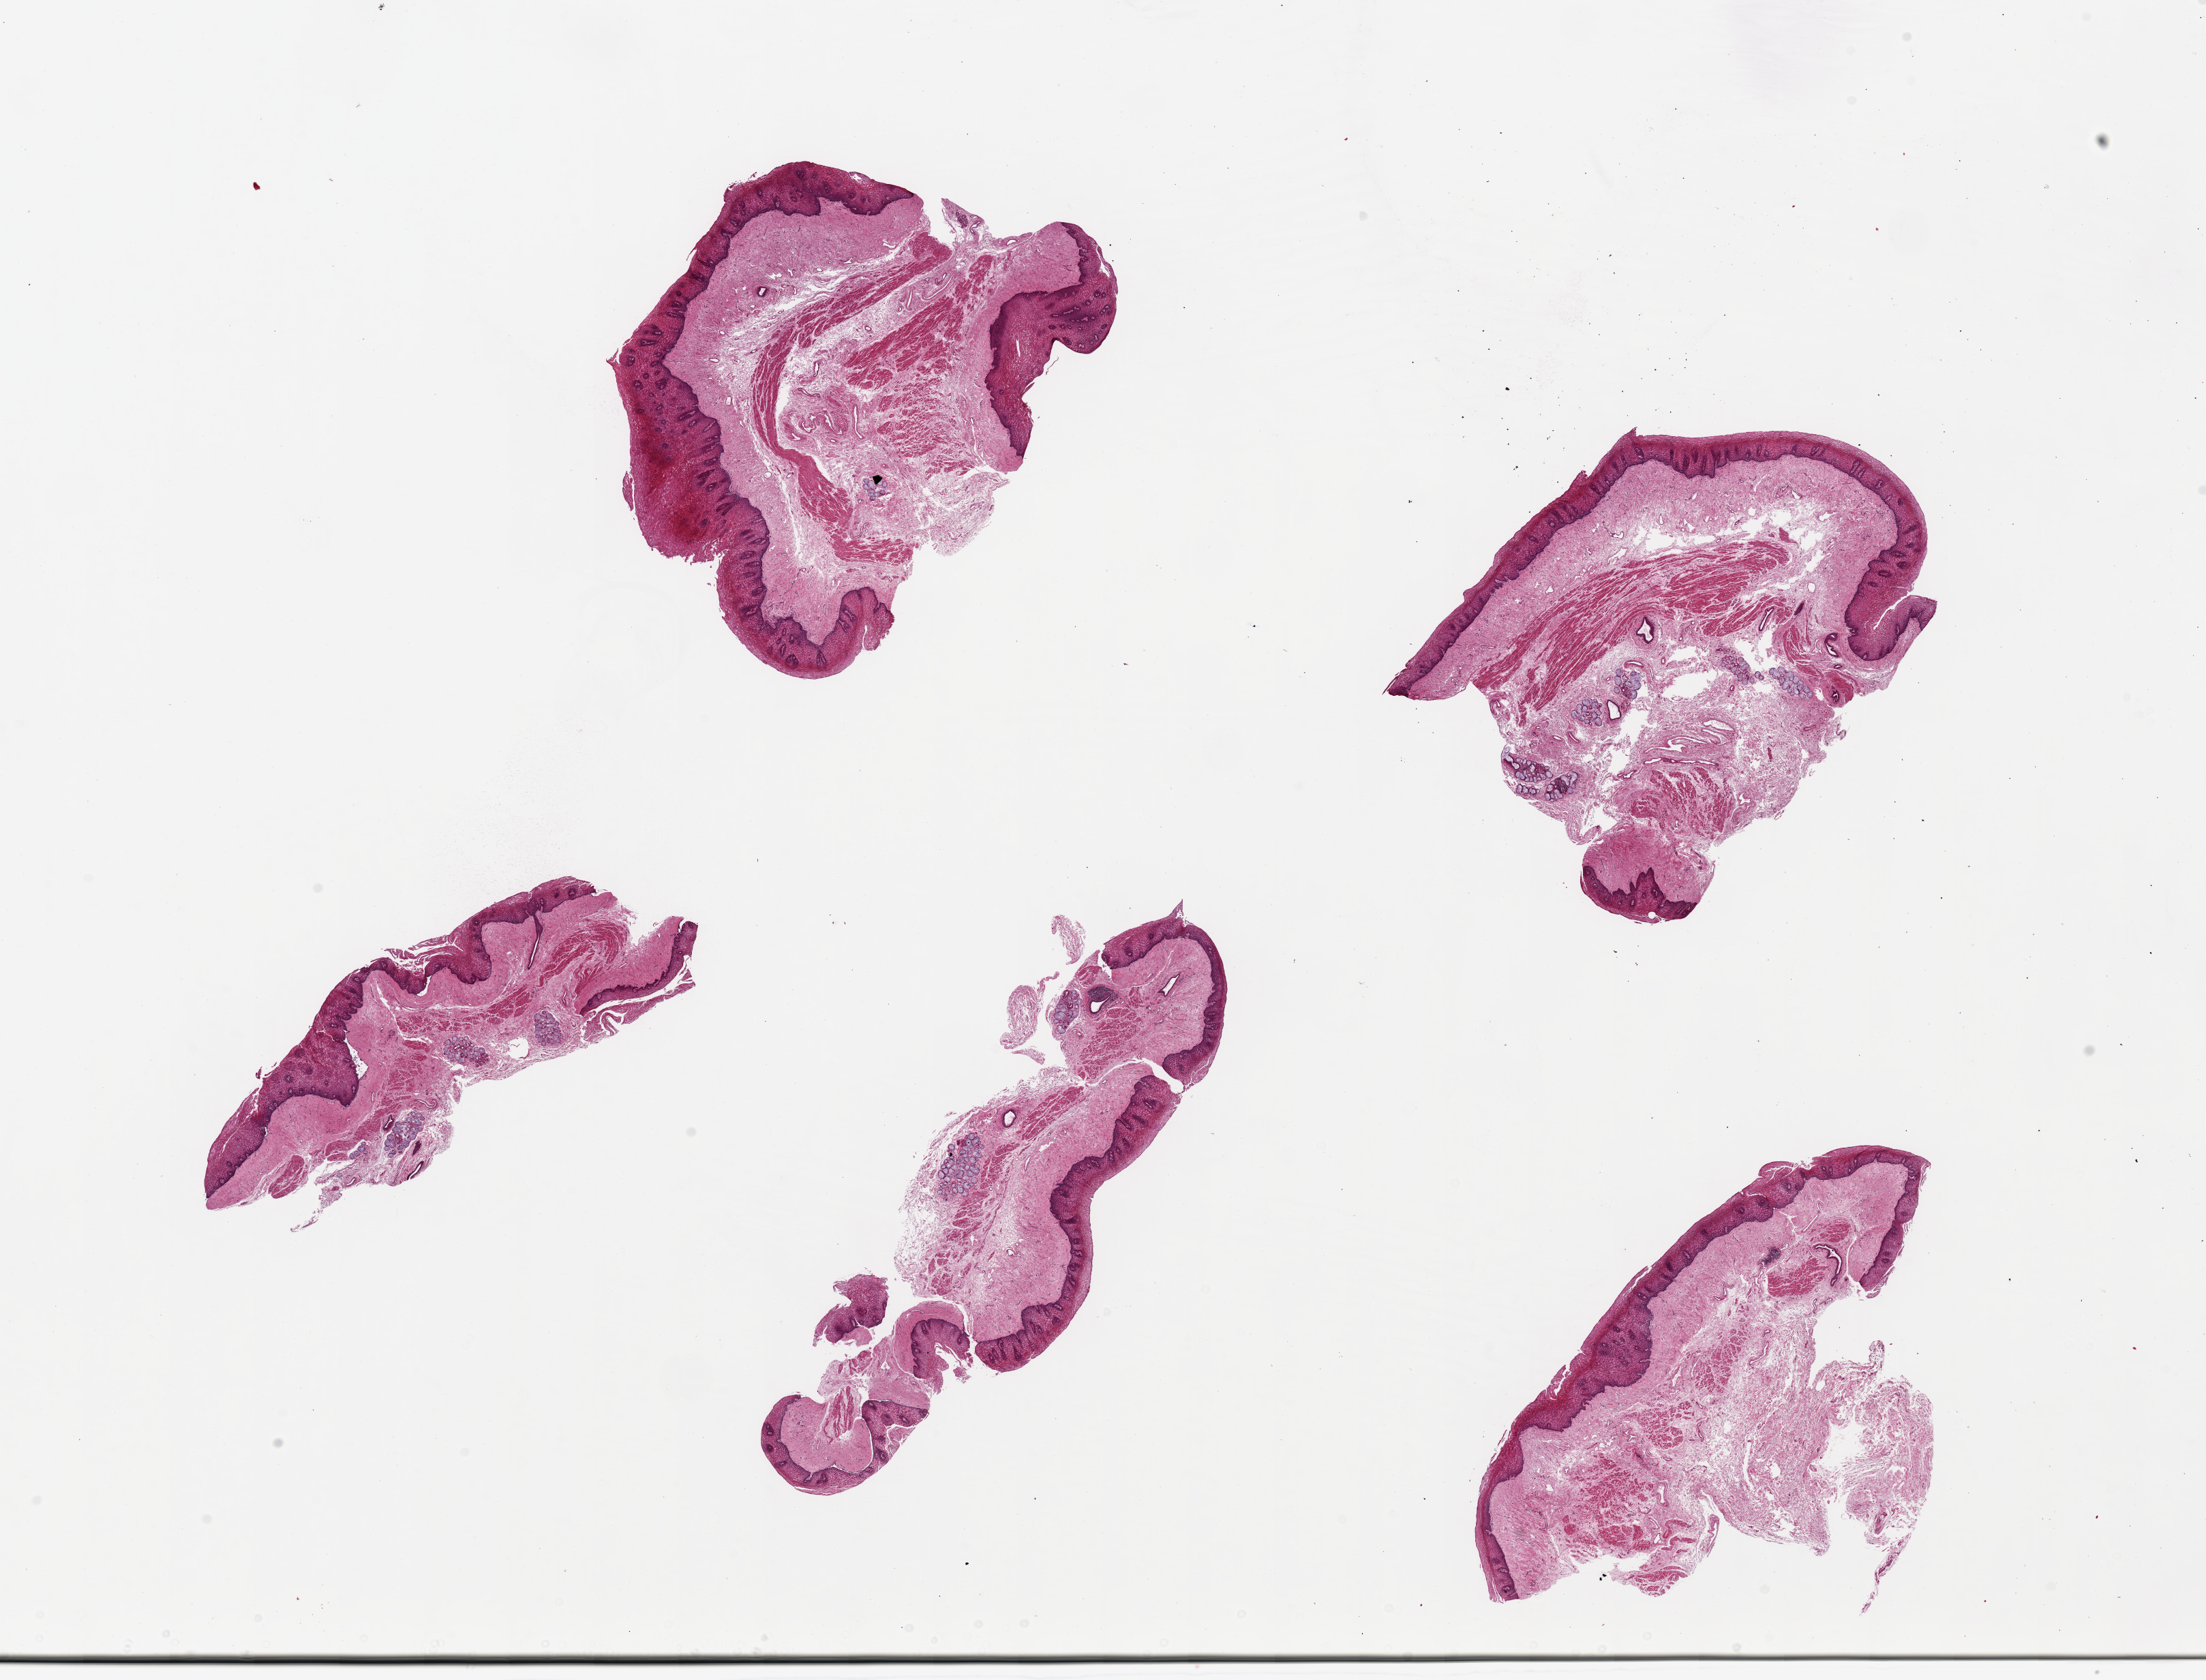
Whole-slide image, H&E stain, brightfield — a low-resolution overview of the entire scanned area, about 25.6 x 19.5 mm, PAXgene-fixed paraffin-embedded (PFPE) section, sampled site (target tissue): esophageal mucous membrane, donor tissue sample. Donor: female.
Reviewer comment on this tissue sample: 5 pieces, up to 8x3mm; all have mucosa.